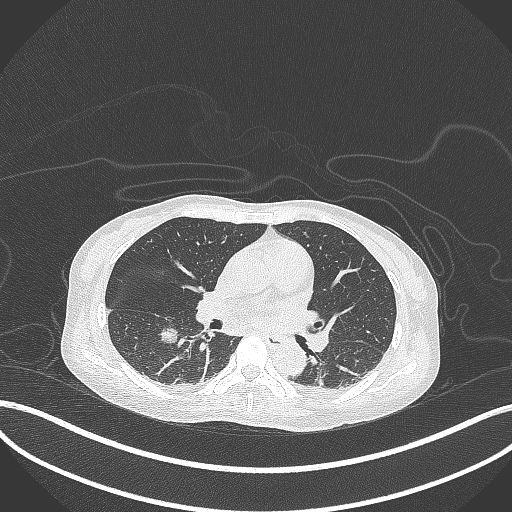
Chest CT, one axial slice; position 163 of 261 along the scan axis; reconstruction kernel B70f; lung window (W 1500 / L -600 HU); 1 mm slice thickness; 512 × 512 image matrix. Female patient, age 44 years. Case-level facts recorded for this patient, not image findings: clinical TNM (as recorded): T1c N0 M0.
Structures marked on this image (rectangle marked by the reading radiologist):
- lung tumour (recorded histology: adenocarcinoma): box from (x=157, y=324) to (x=180, y=346) px